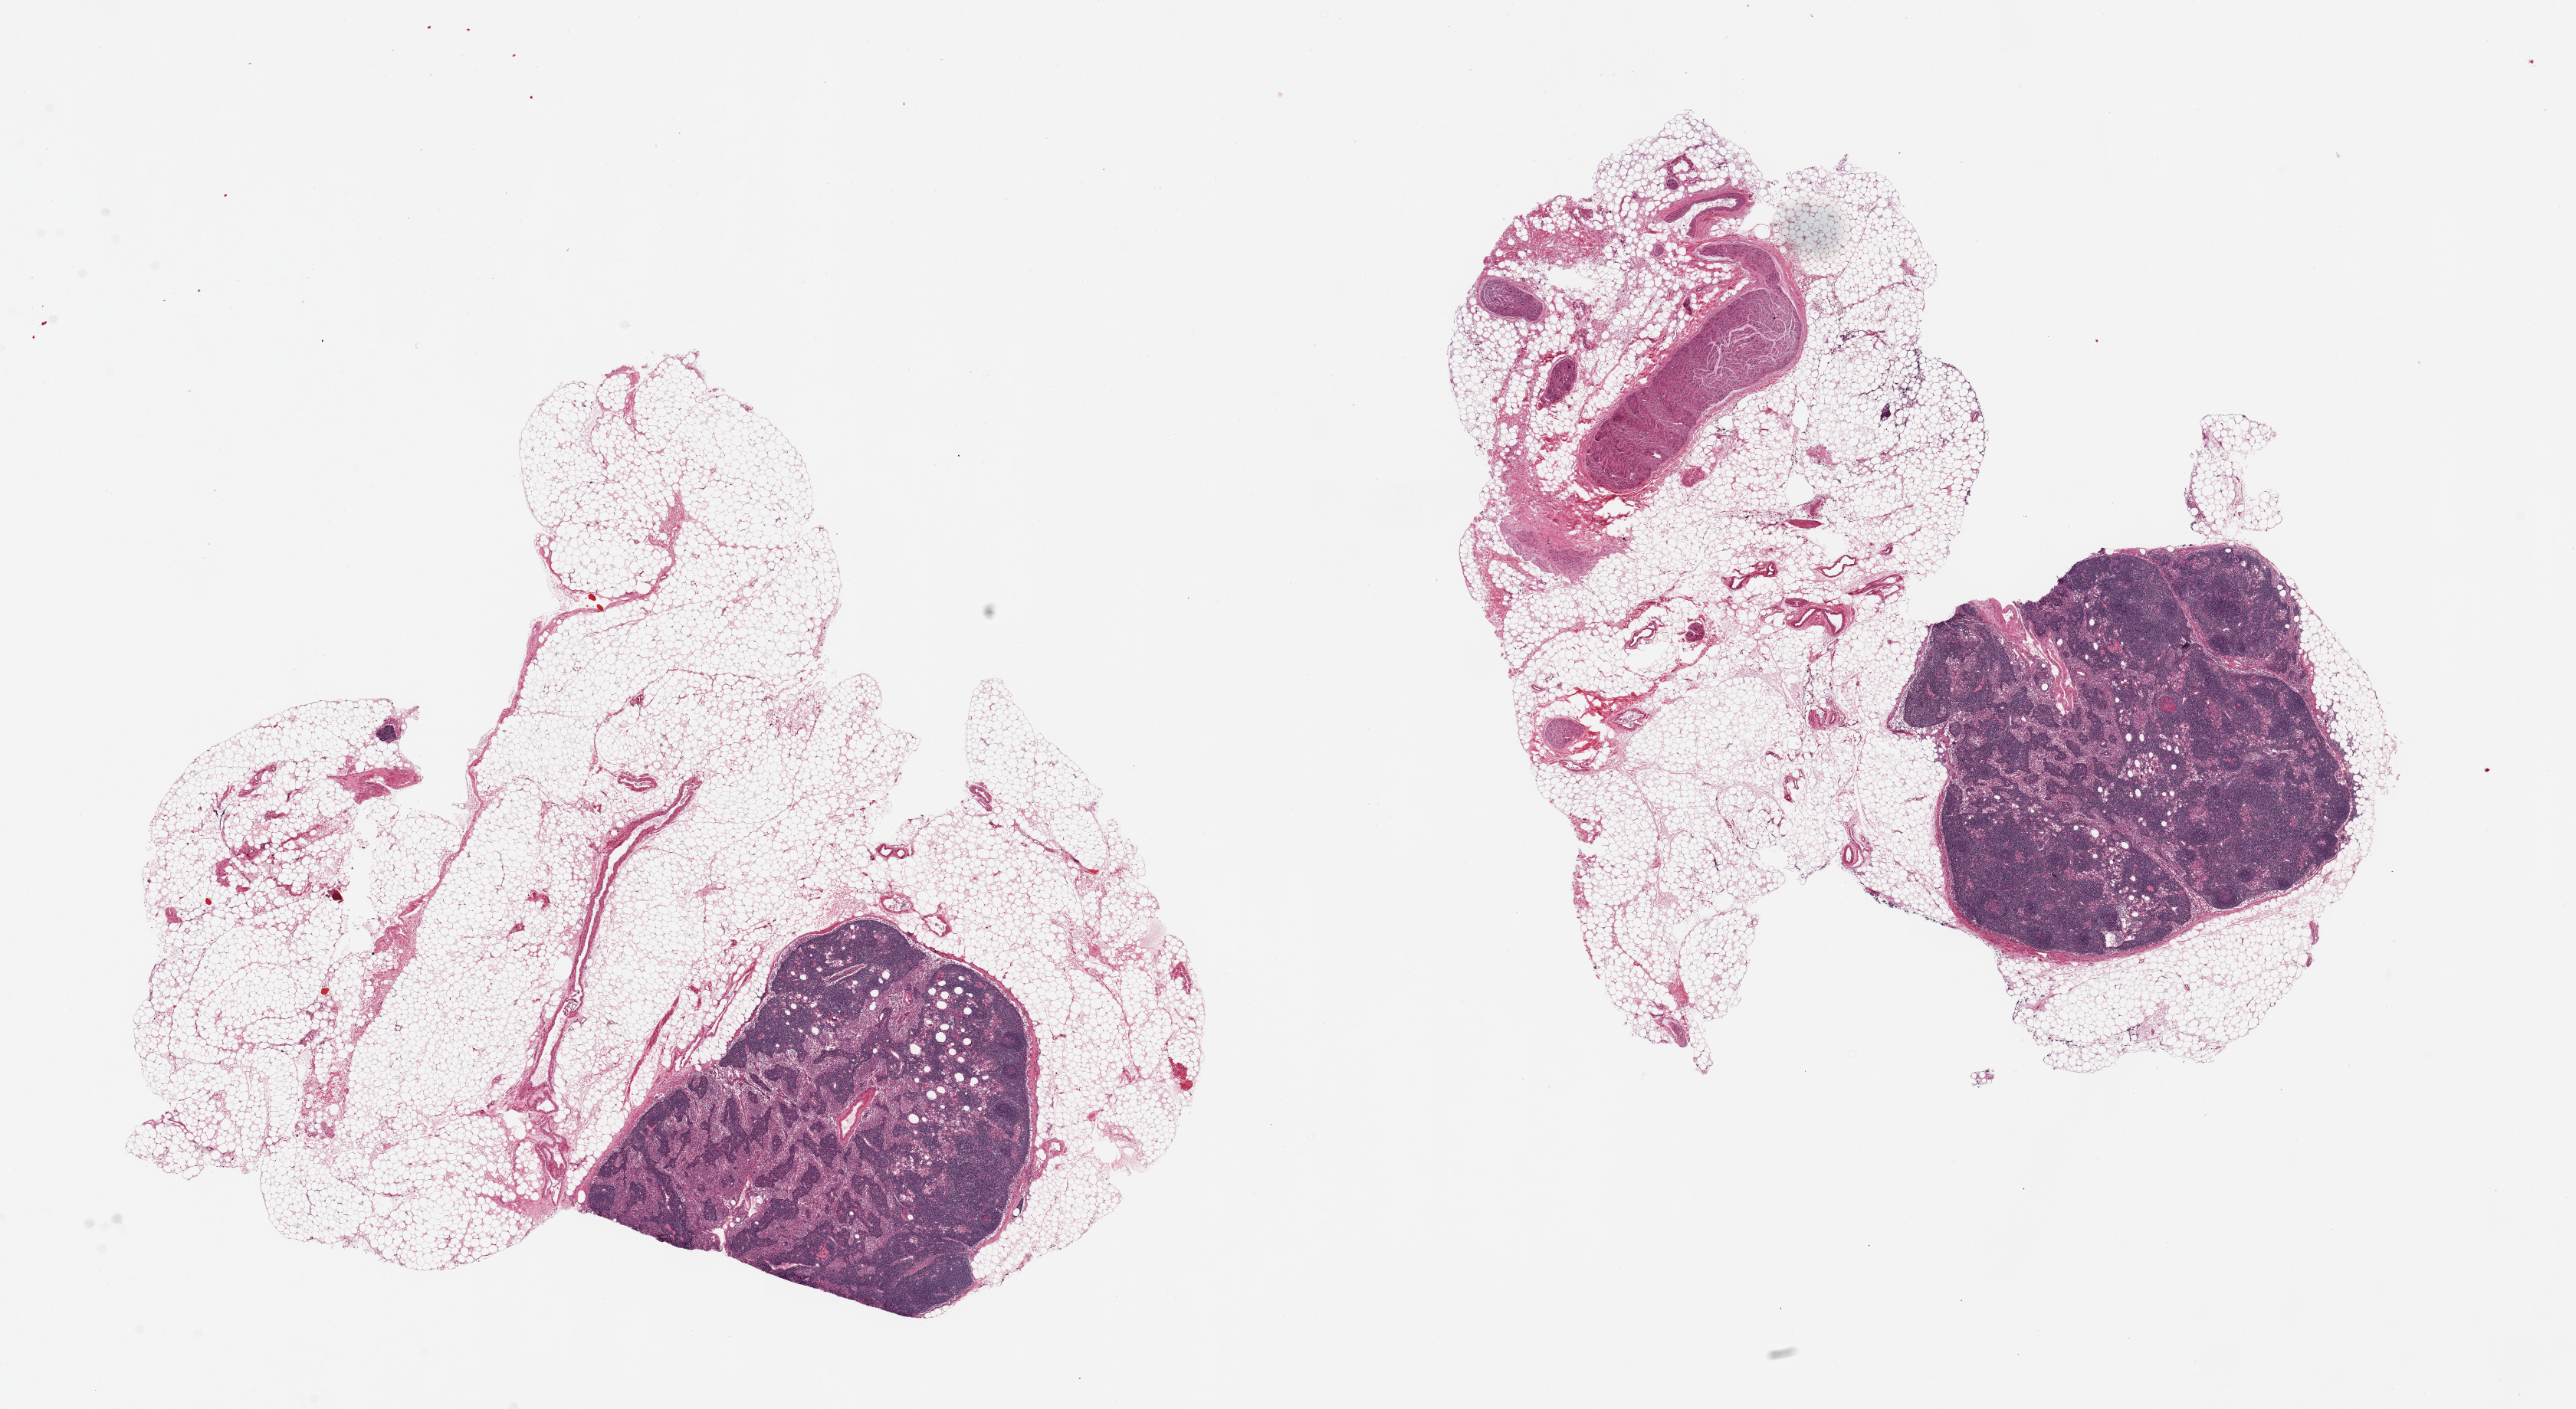
Whole-slide image, hematoxylin and eosin (H&E) stain, shown as a low-resolution overview of the whole scanned area (about 26.6 x 14.5 mm, slide scanned at 20x). PAXgene-fixed paraffin-embedded (PFPE) section. Sampled site (target tissue): pancreas. Donor tissue sample. Donor sex: male.
Reviewer comment on this tissue sample: 2 pieces, not pancreas; lymph nodes and fat.